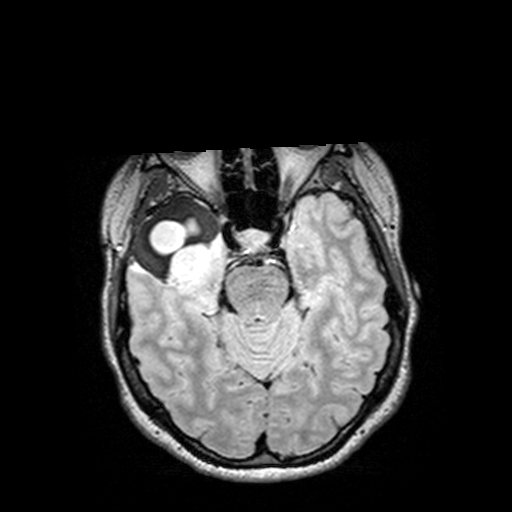
Brain MRI from a brain-tumour surgery series, one axial slice; slice 95 of 144 in the series (ordered by position); T2 FLAIR; 1 mm slice thickness; 512 × 512 image matrix, field of view 250 × 250 mm. Case-level facts recorded for this patient, not image findings: histopathology: Astrocytoma; WHO grade: 3.
Structures marked on this image (expert manual segmentation):
- tumour: bounding box (x1, y1, x2, y2) in pixels: (126, 194, 232, 286)